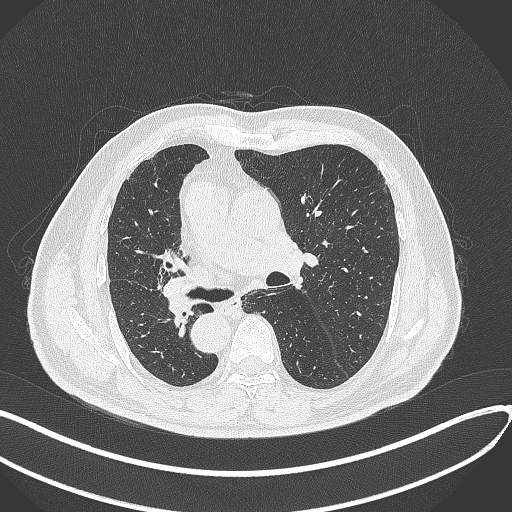
Chest CT, one axial slice. Lung window (W 1500 / L -600 HU). 1 mm slice thickness. 512 × 512 image matrix. Male patient, age 67 years. From the clinical record (not read from this slice): clinical TNM (as recorded): T2a N0 M0.
Outlined on this slice (bounding box drawn by a radiologist):
- lung tumour (recorded histology: squamous cell carcinoma): bounding box <158,280,203,327> (left, top, right, bottom; pixels)